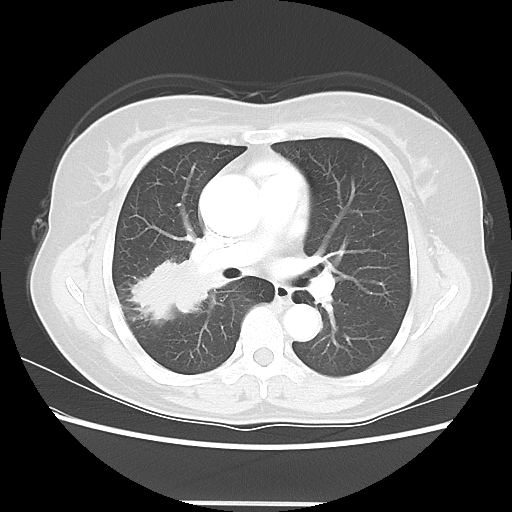
Chest CT, one axial slice. Slice 34 of 56 in the series (ordered by position). Lung window (W 1500 / L -600 HU). 512 × 512 image matrix. Female patient, age 55 years. Case-level facts recorded for this patient, not image findings: clinical TNM (as recorded): T2 N1 M0; histopathological grade: G2-3.
Annotated regions visible in this slice (rectangle marked by the reading radiologist):
- lung tumour (recorded histology: adenocarcinoma): bounding box <125,250,225,330> (left, top, right, bottom; pixels)